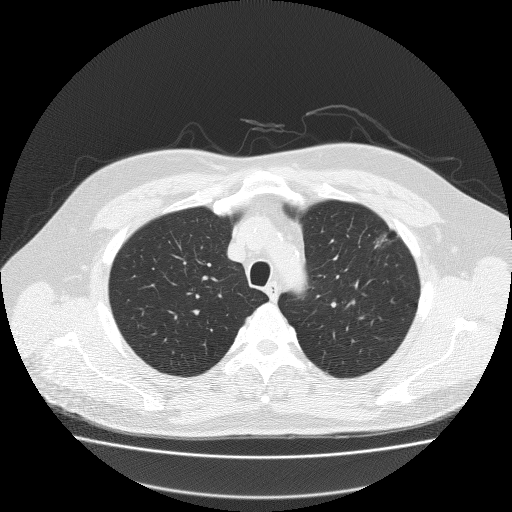
Axial slice from a low-dose chest CT screening exam. Baseline screening round. Lung window (W 1500 / L -600 HU). 2 mm slice thickness. Lung (sharp) reconstruction kernel (FC51). 512 × 512 image matrix. Male, age 62 years at enrolment. Former smoker at enrolment.
Expert reader's lesion annotation, bounding box [x1, y1, x2, y2] px = [346, 219, 413, 269]. The exam's reader record, not a measurement of the box and not confirmed to be the same lesion: non-calcified nodule or mass ≥4 mm, left upper lobe, 18 × 8 mm, spiculated (stellate) margins, soft tissue attenuation. Official screen result: positive, change unspecified: nodule(s) >= 4 mm or enlarging nodule(s), mass(es), or other non-specific abnormalities suspicious for lung cancer. Participant outcome: lung cancer diagnosed 49 days after this screen — bronchiolo-alveolar adenocarcinoma, NOS, left upper lobe, well differentiated (G1), stage IA (AJCC 6th edition), 25 mm at pathology.